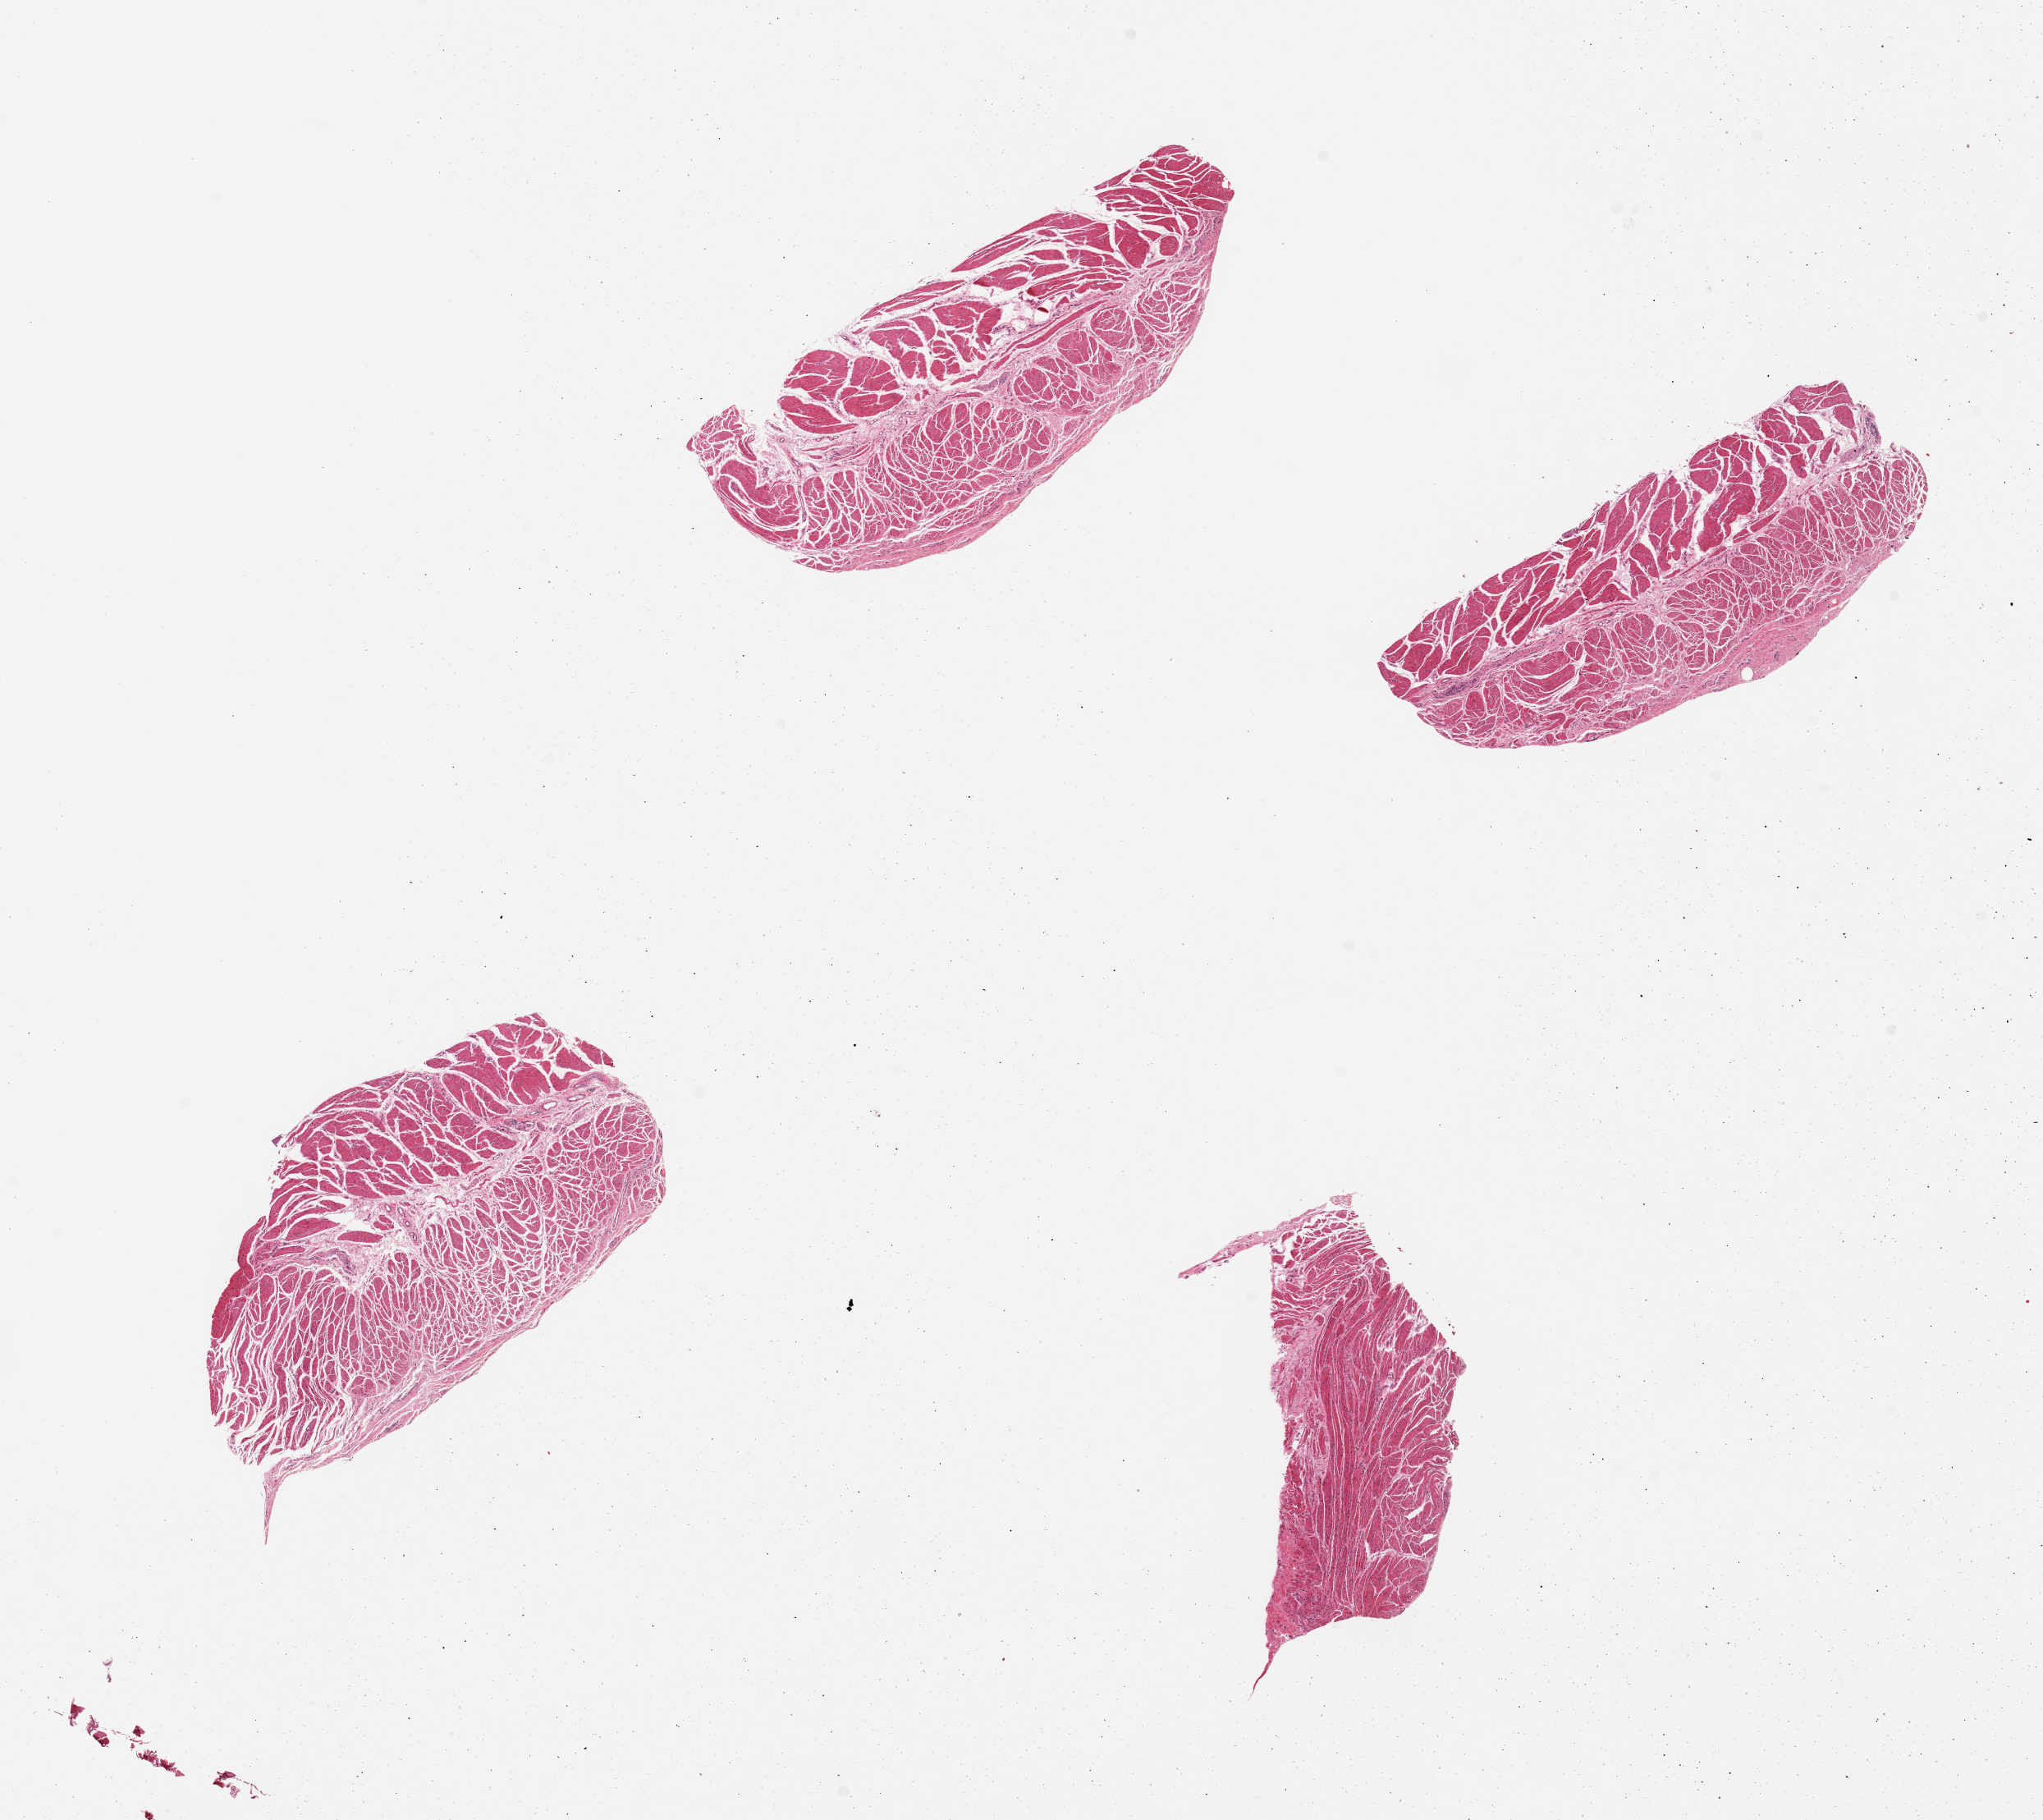
H&E whole-slide image — low-resolution overview of the scanned area, about 19.7 x 17.5 mm. PAXgene-fixed paraffin-embedded (PFPE) section. Section of esophageal muscle (target tissue). Donor tissue sample.
Review note (as recorded): 4 pieces; no sign of fibrosis.